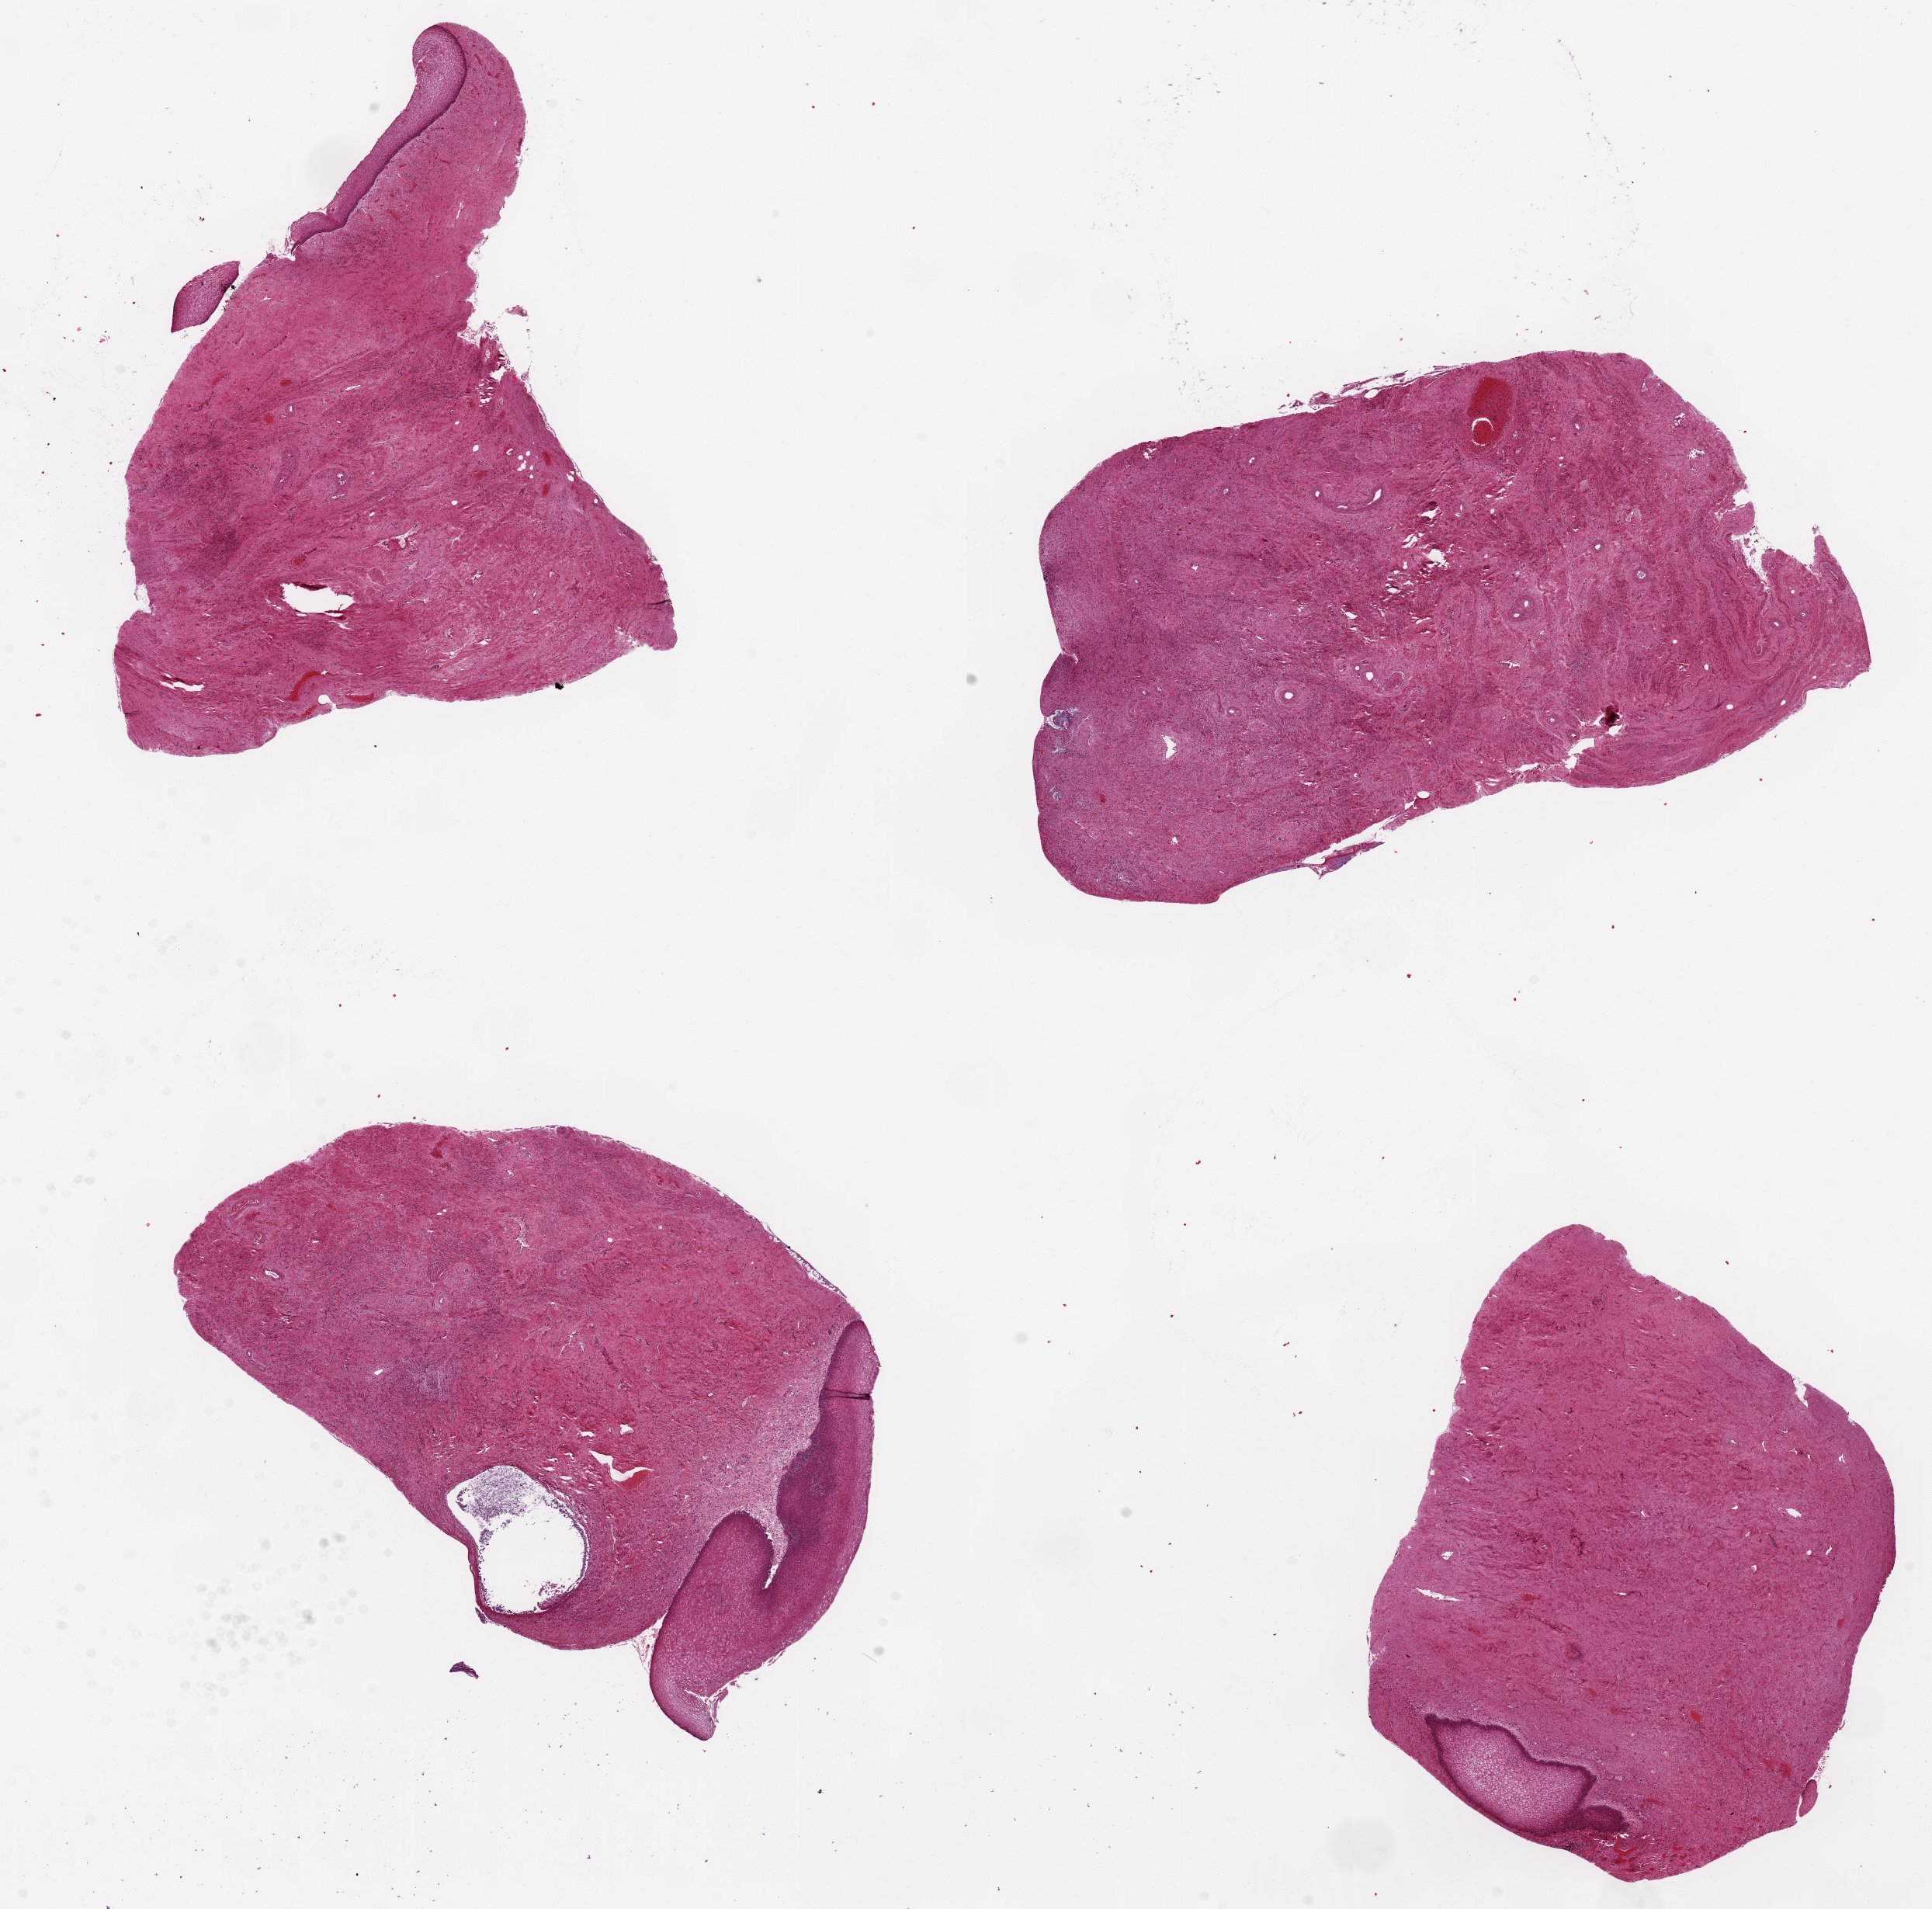
H&E whole-slide image — a low-resolution overview of the entire scanned area, about 19.7 x 19.5 mm (acquisition: 20x scan), PAXgene-fixed paraffin-embedded (PFPE) section, sampled site (target tissue): exocervix, donor tissue sample. Donor: female.
- pathologist's review note for this sample: 4 ~7x5mm aliquots, few minute foci of squamous mucosa present